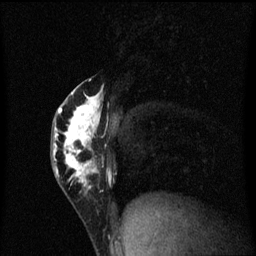
Breast MRI (dynamic contrast-enhanced), one sagittal slice; position 28 of 60 along the scan axis; dynamic contrast-enhanced series, image 2 of 3 at this slice position (ordered by acquisition); 1.5 T; TE 4.2 ms, TR 8.4 ms; 2 mm slice thickness; 256 × 256 image matrix. Female patient, age 40 years.
Annotated regions visible in this slice (semi-automatic segmentation, software-assisted and operator-edited):
- analysis volume of interest (the breast-tissue region the enhancement analysis was run in; not a lesion): bounding box (x1, y1, x2, y2) in pixels: (52, 78, 110, 203)
- tumour enhancement mask (voxels above the 70 % enhancement threshold inside the analysis volume of interest): (54, 80, 110, 189)